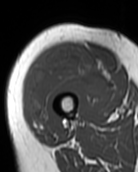
MRI of an extremity soft-tissue mass, one axial slice. Slice 32 of 99 in the series (ordered by position). MR volume resampled by the dataset authors to the PET/CT grid (not the native acquisition matrix). 3.27 mm slice thickness. 138 × 172 image matrix, field of view 135 × 168 mm. Female patient. Case-level facts recorded for this patient, not image findings: histological type: pleiomorphic undifferentiated sarcoma; grade: high; site of the primary tumour: right quadricep.
Structures marked on this image (expert contour drawn on MRI and transferred to this co-registered scan by the dataset authors):
- gross tumour volume including surrounding oedema: bounding box (x1, y1, x2, y2) in pixels: (25, 48, 109, 131)
- gross tumour volume (mass): (25, 48, 109, 131)